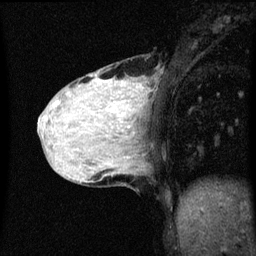
Breast MRI (dynamic contrast-enhanced), one sagittal slice; slice 19 of 60 in the series (ordered by position); dynamic contrast-enhanced series, image 2 of 3 at this slice position (ordered by acquisition); 1.5 T; TE 4.2 ms, TR 8.4 ms; 2 mm slice thickness; 256 × 256 image matrix. Female patient, age 36 years.
Annotated regions visible in this slice (semi-automatically segmented with operator editing):
- analysis volume of interest (the breast-tissue region the enhancement analysis was run in; not a lesion): box from (x=48, y=66) to (x=151, y=151) px
- tumour enhancement mask (voxels above the 70 % enhancement threshold inside the analysis volume of interest): (x=112, y=86)–(x=145, y=129)